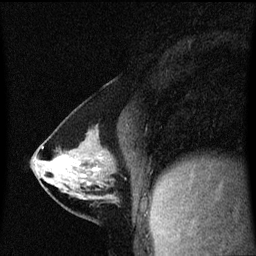
Breast MRI (dynamic contrast-enhanced), one sagittal slice; position 27 of 60 along the scan axis; dynamic contrast-enhanced series, image 2 of 3 at this slice position (ordered by acquisition); 1.5 T; TE 4.2 ms, TR 8.4 ms; 256 × 256 image matrix, field of view 200 × 200 mm. Female patient, age 40 years. From the clinical record (not read from this slice): setting: breast cancer imaged before/during neoadjuvant chemotherapy; receptor status: triple-negative.
Structures marked on this image (semi-automatically segmented with operator editing):
- analysis volume of interest (the breast-tissue region the enhancement analysis was run in; not a lesion): bounding box [x1, y1, x2, y2] px = [34, 142, 117, 199]
- tumour enhancement mask (voxels above the 70 % enhancement threshold inside the analysis volume of interest): [55, 154, 99, 177]